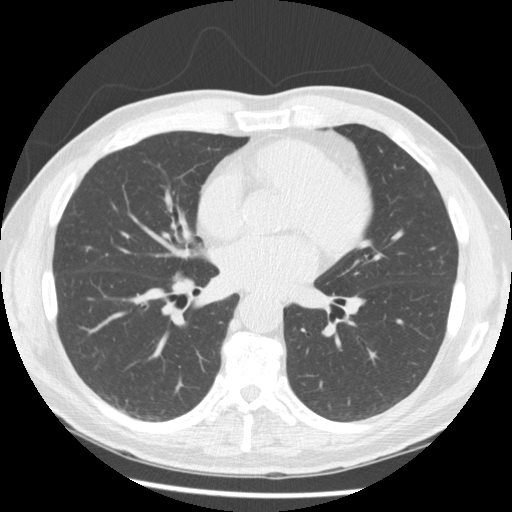
Low-dose screening chest CT, axial slice; baseline screening round; lung window (W 1500 / L -600 HU); 2.5 mm slice thickness; standard (soft-tissue) reconstruction kernel (STANDARD); 120 kVp; slice 85 of 166 in the series. Male, age 62 years at enrolment. Current smoker at enrolment.
Lesion marked by an expert reader, bounding box <151,256,213,312> (left, top, right, bottom; pixels). Screening reader's record for this exam: no non-calcified nodule ≥4 mm recorded. Official screen result: negative screen, minor abnormalities not suspicious for lung cancer. Later outcome: lung cancer diagnosed 146 days after this screen — small cell carcinoma, NOS, right hilum, mediastinum, poorly differentiated (G3), stage IV (AJCC 6th edition).